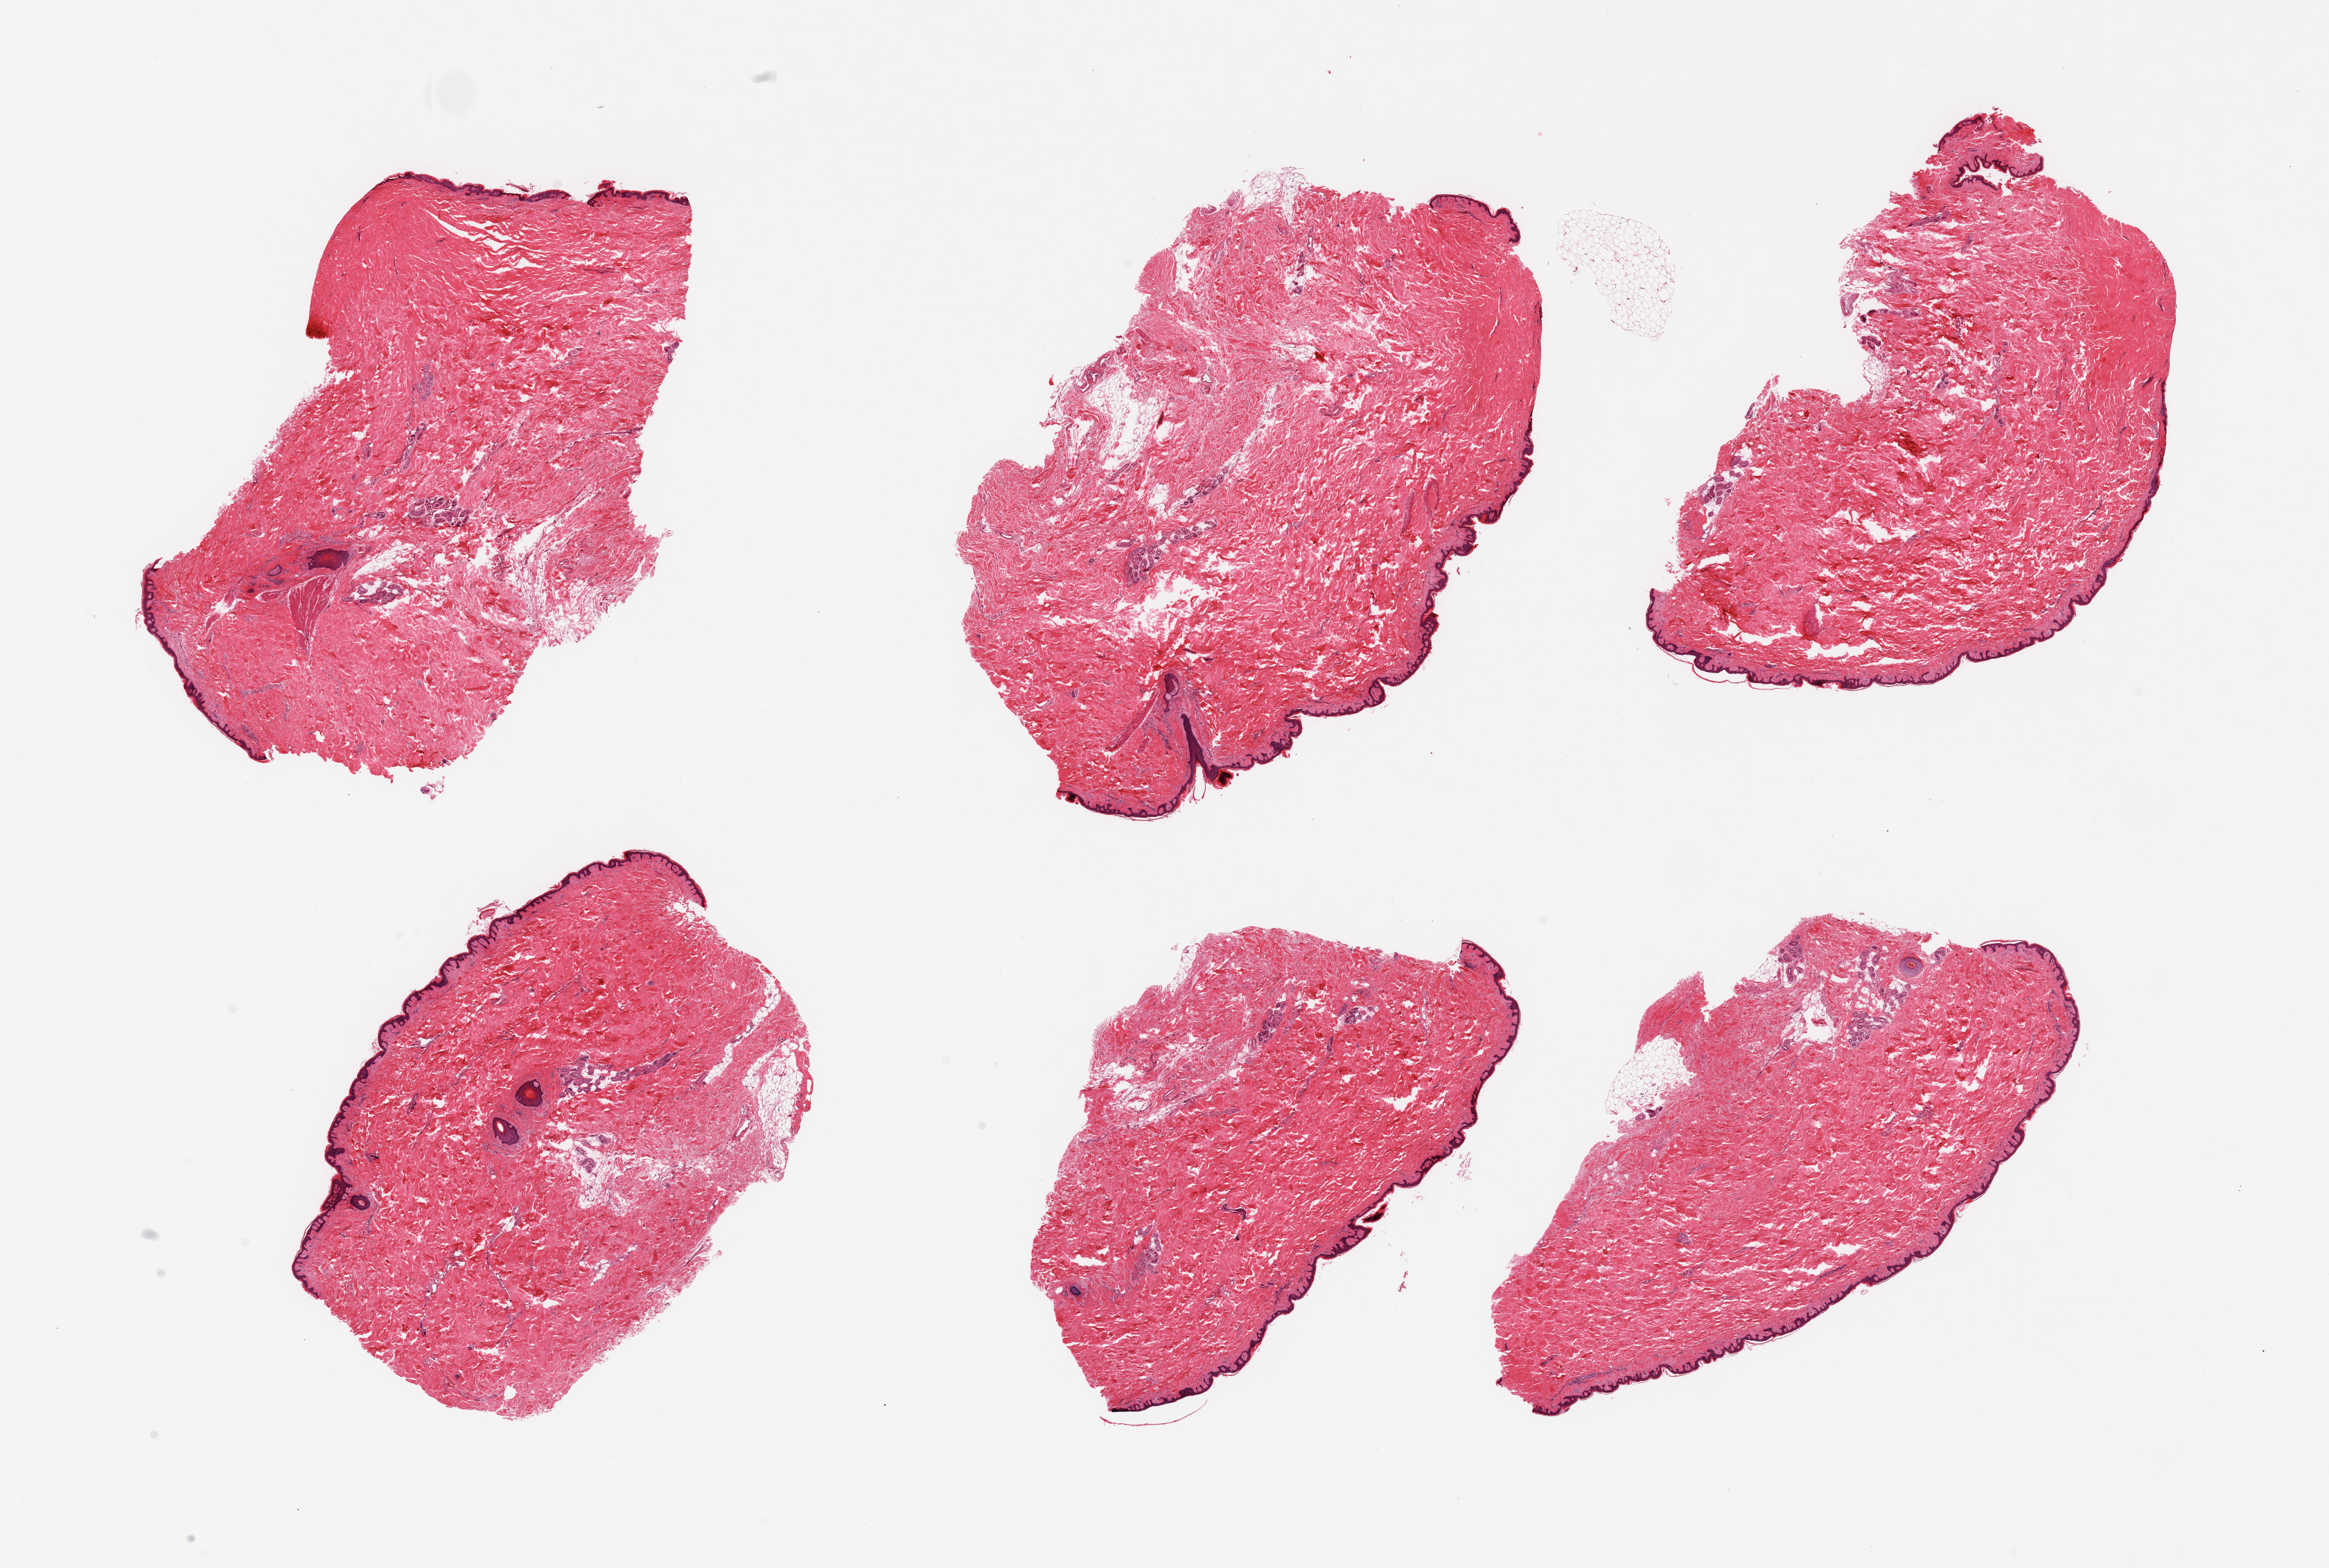
H&E whole-slide image — a low-resolution overview of the entire scanned area, about 26.6 x 17.9 mm (from a 20x scan), PAXgene-fixed paraffin-embedded (PFPE) section, sampled site (target tissue): skin of suprapubic region, donor tissue sample. Donor: male.
Pathologist's review note for this sample: 6 pieces; <5% dermal fat; well trimmed.